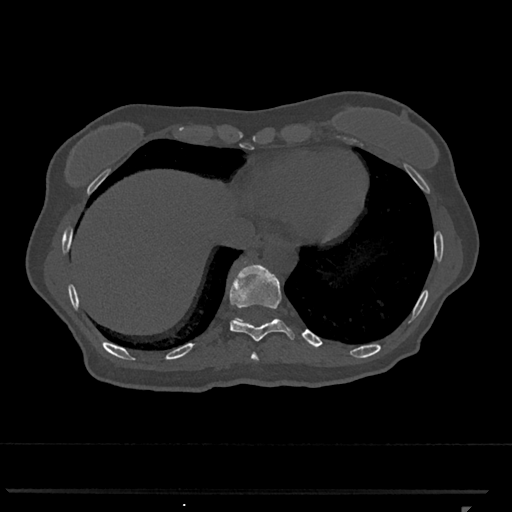
CT including the spine, one axial slice; reconstruction kernel Br40s/3; bone window (W 1800 / L 400 HU); 0.5 mm slice thickness; 512 × 512 image matrix, field of view 380 × 380 mm. Patient: female, 62 years. Case-level facts recorded for this patient, not image findings: primary cancer: renal.
Structures marked on this image (semi-automatic segmentation, software-assisted and operator-edited):
- T10 vertebra: bounding box [x1, y1, x2, y2] px = [230, 263, 295, 342]
- T11 vertebra: [233, 307, 272, 322]
- T9 vertebra: [251, 353, 258, 361]